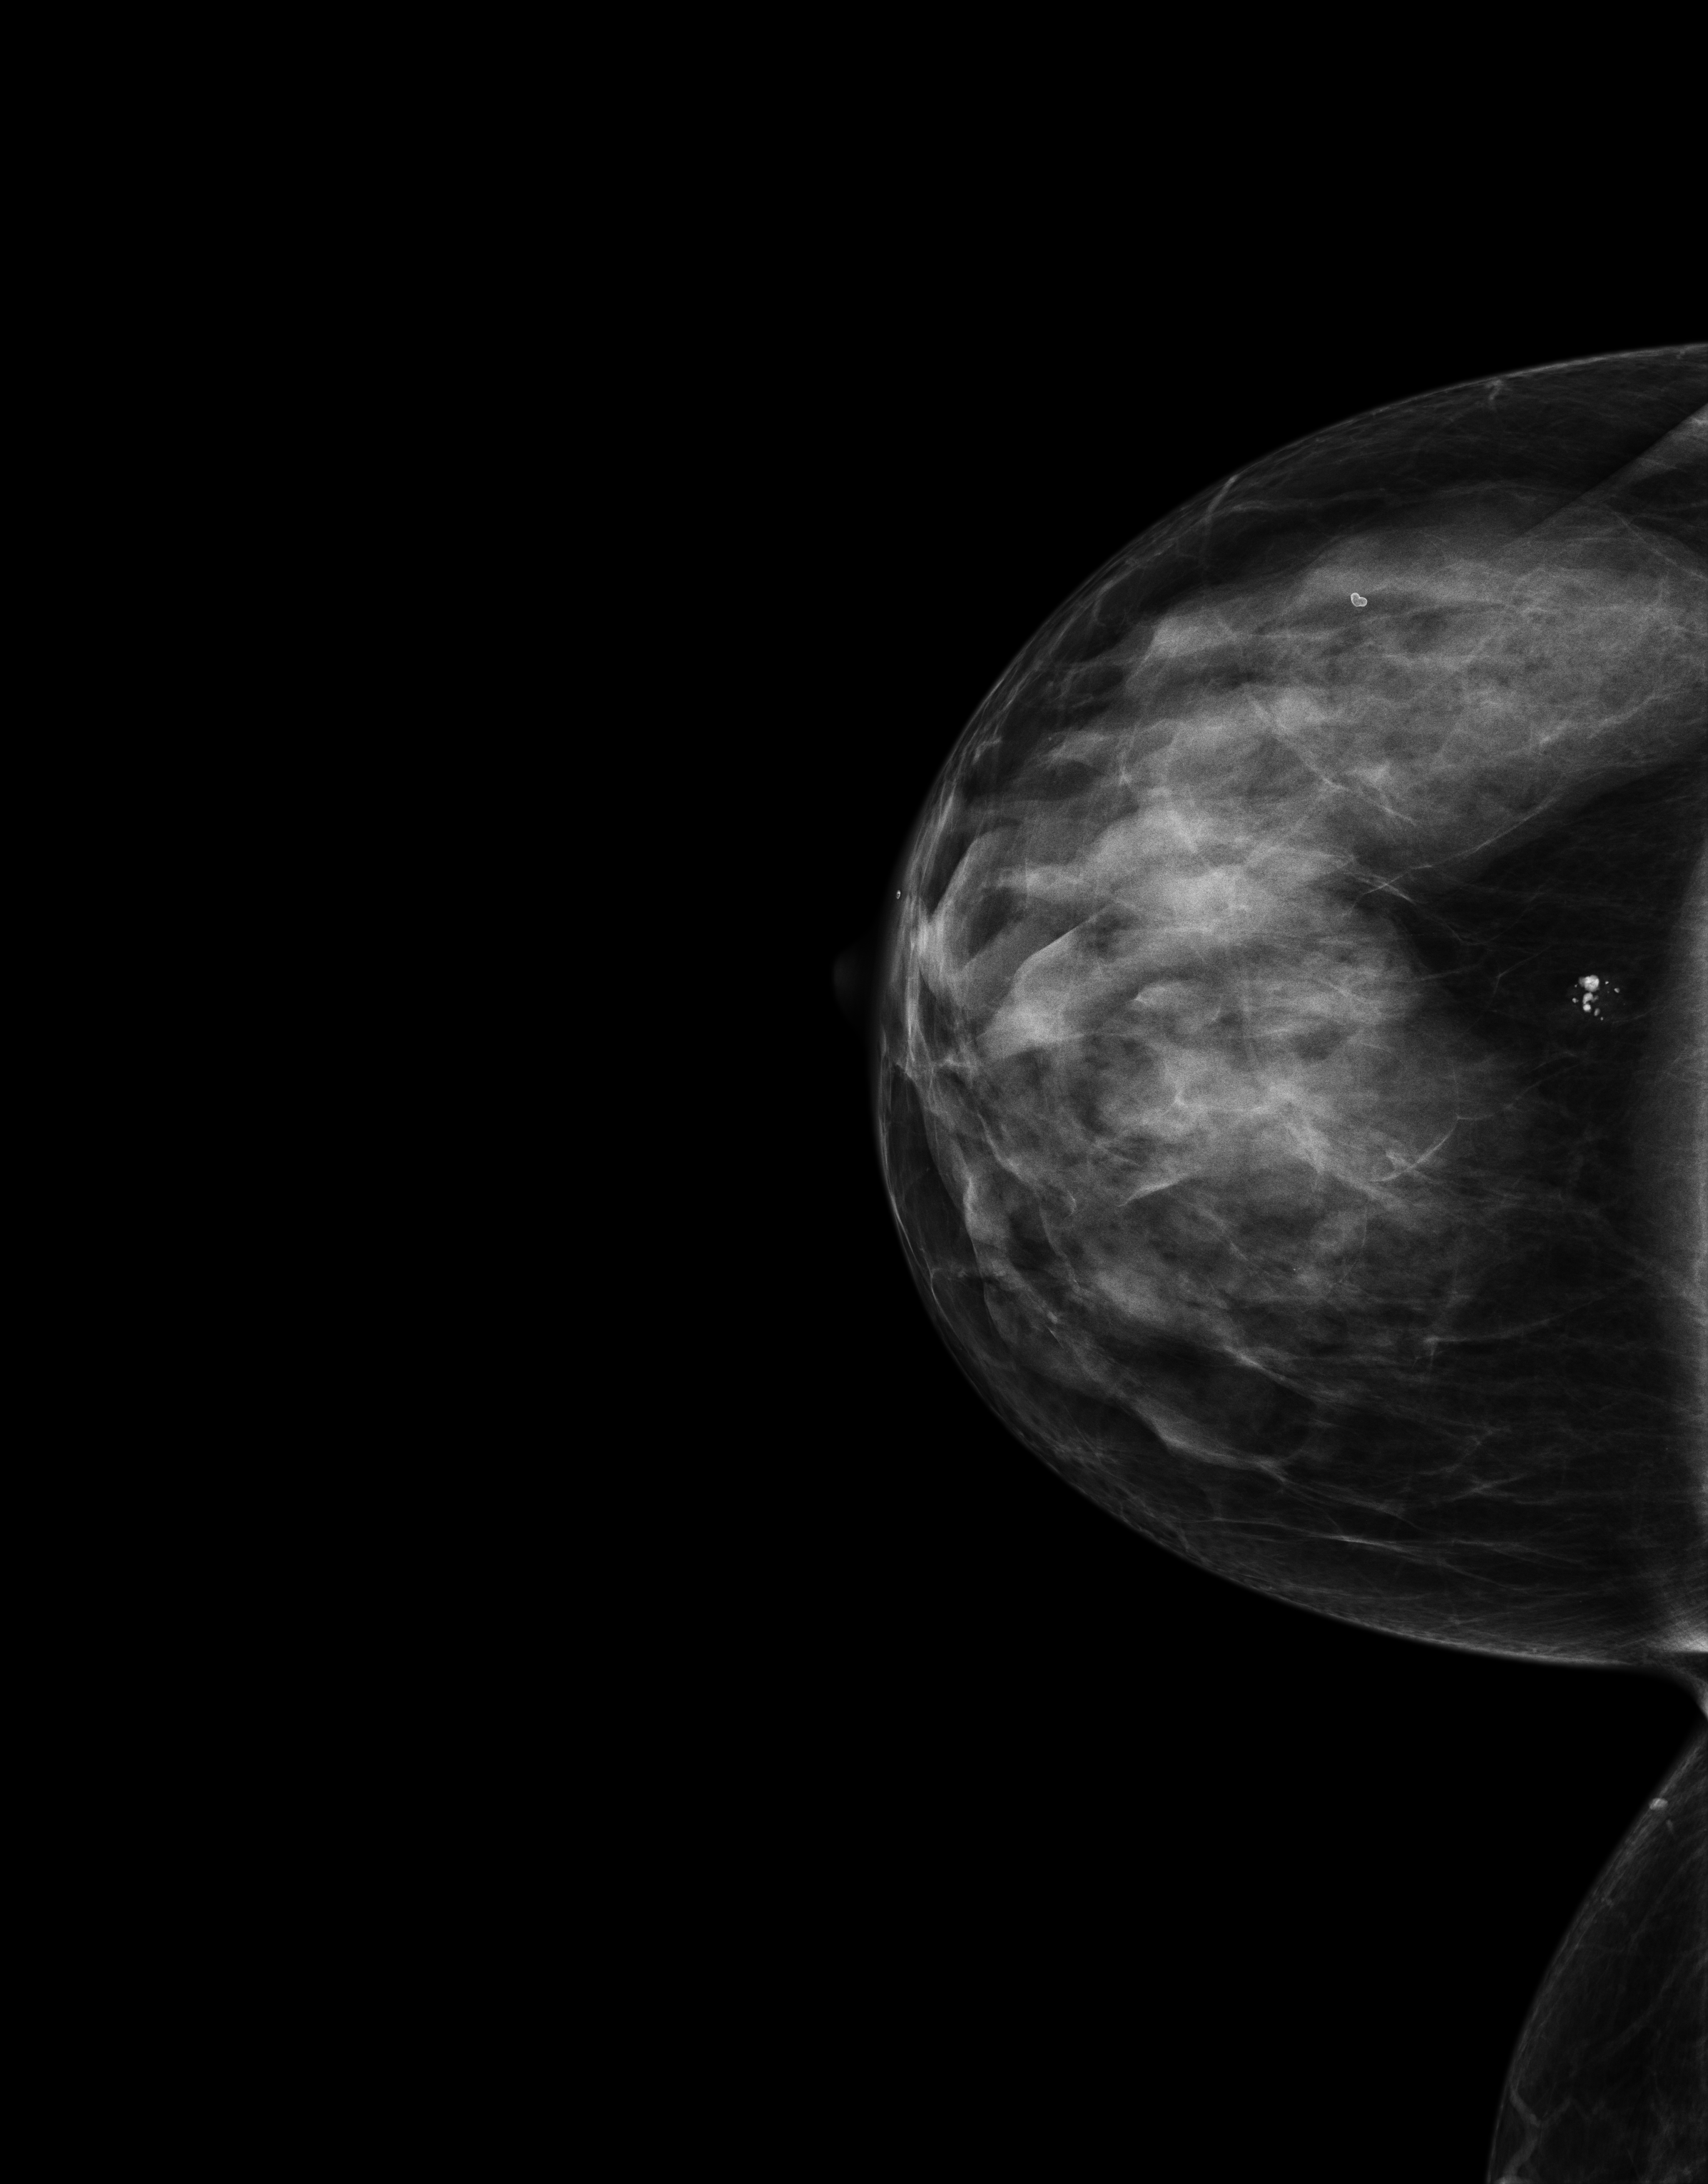
Full-field digital mammogram (FFDM), right breast, craniocaudal (CC) view, annual screening mammography examination. Patient aged 60 years (female).
Breast density at the screening exam (both breasts): extremely dense (BI-RADS density category d). Final BI-RADS category for the screening round (tomosynthesis exam, both breasts): category 1. Recall: no recall after this screen.